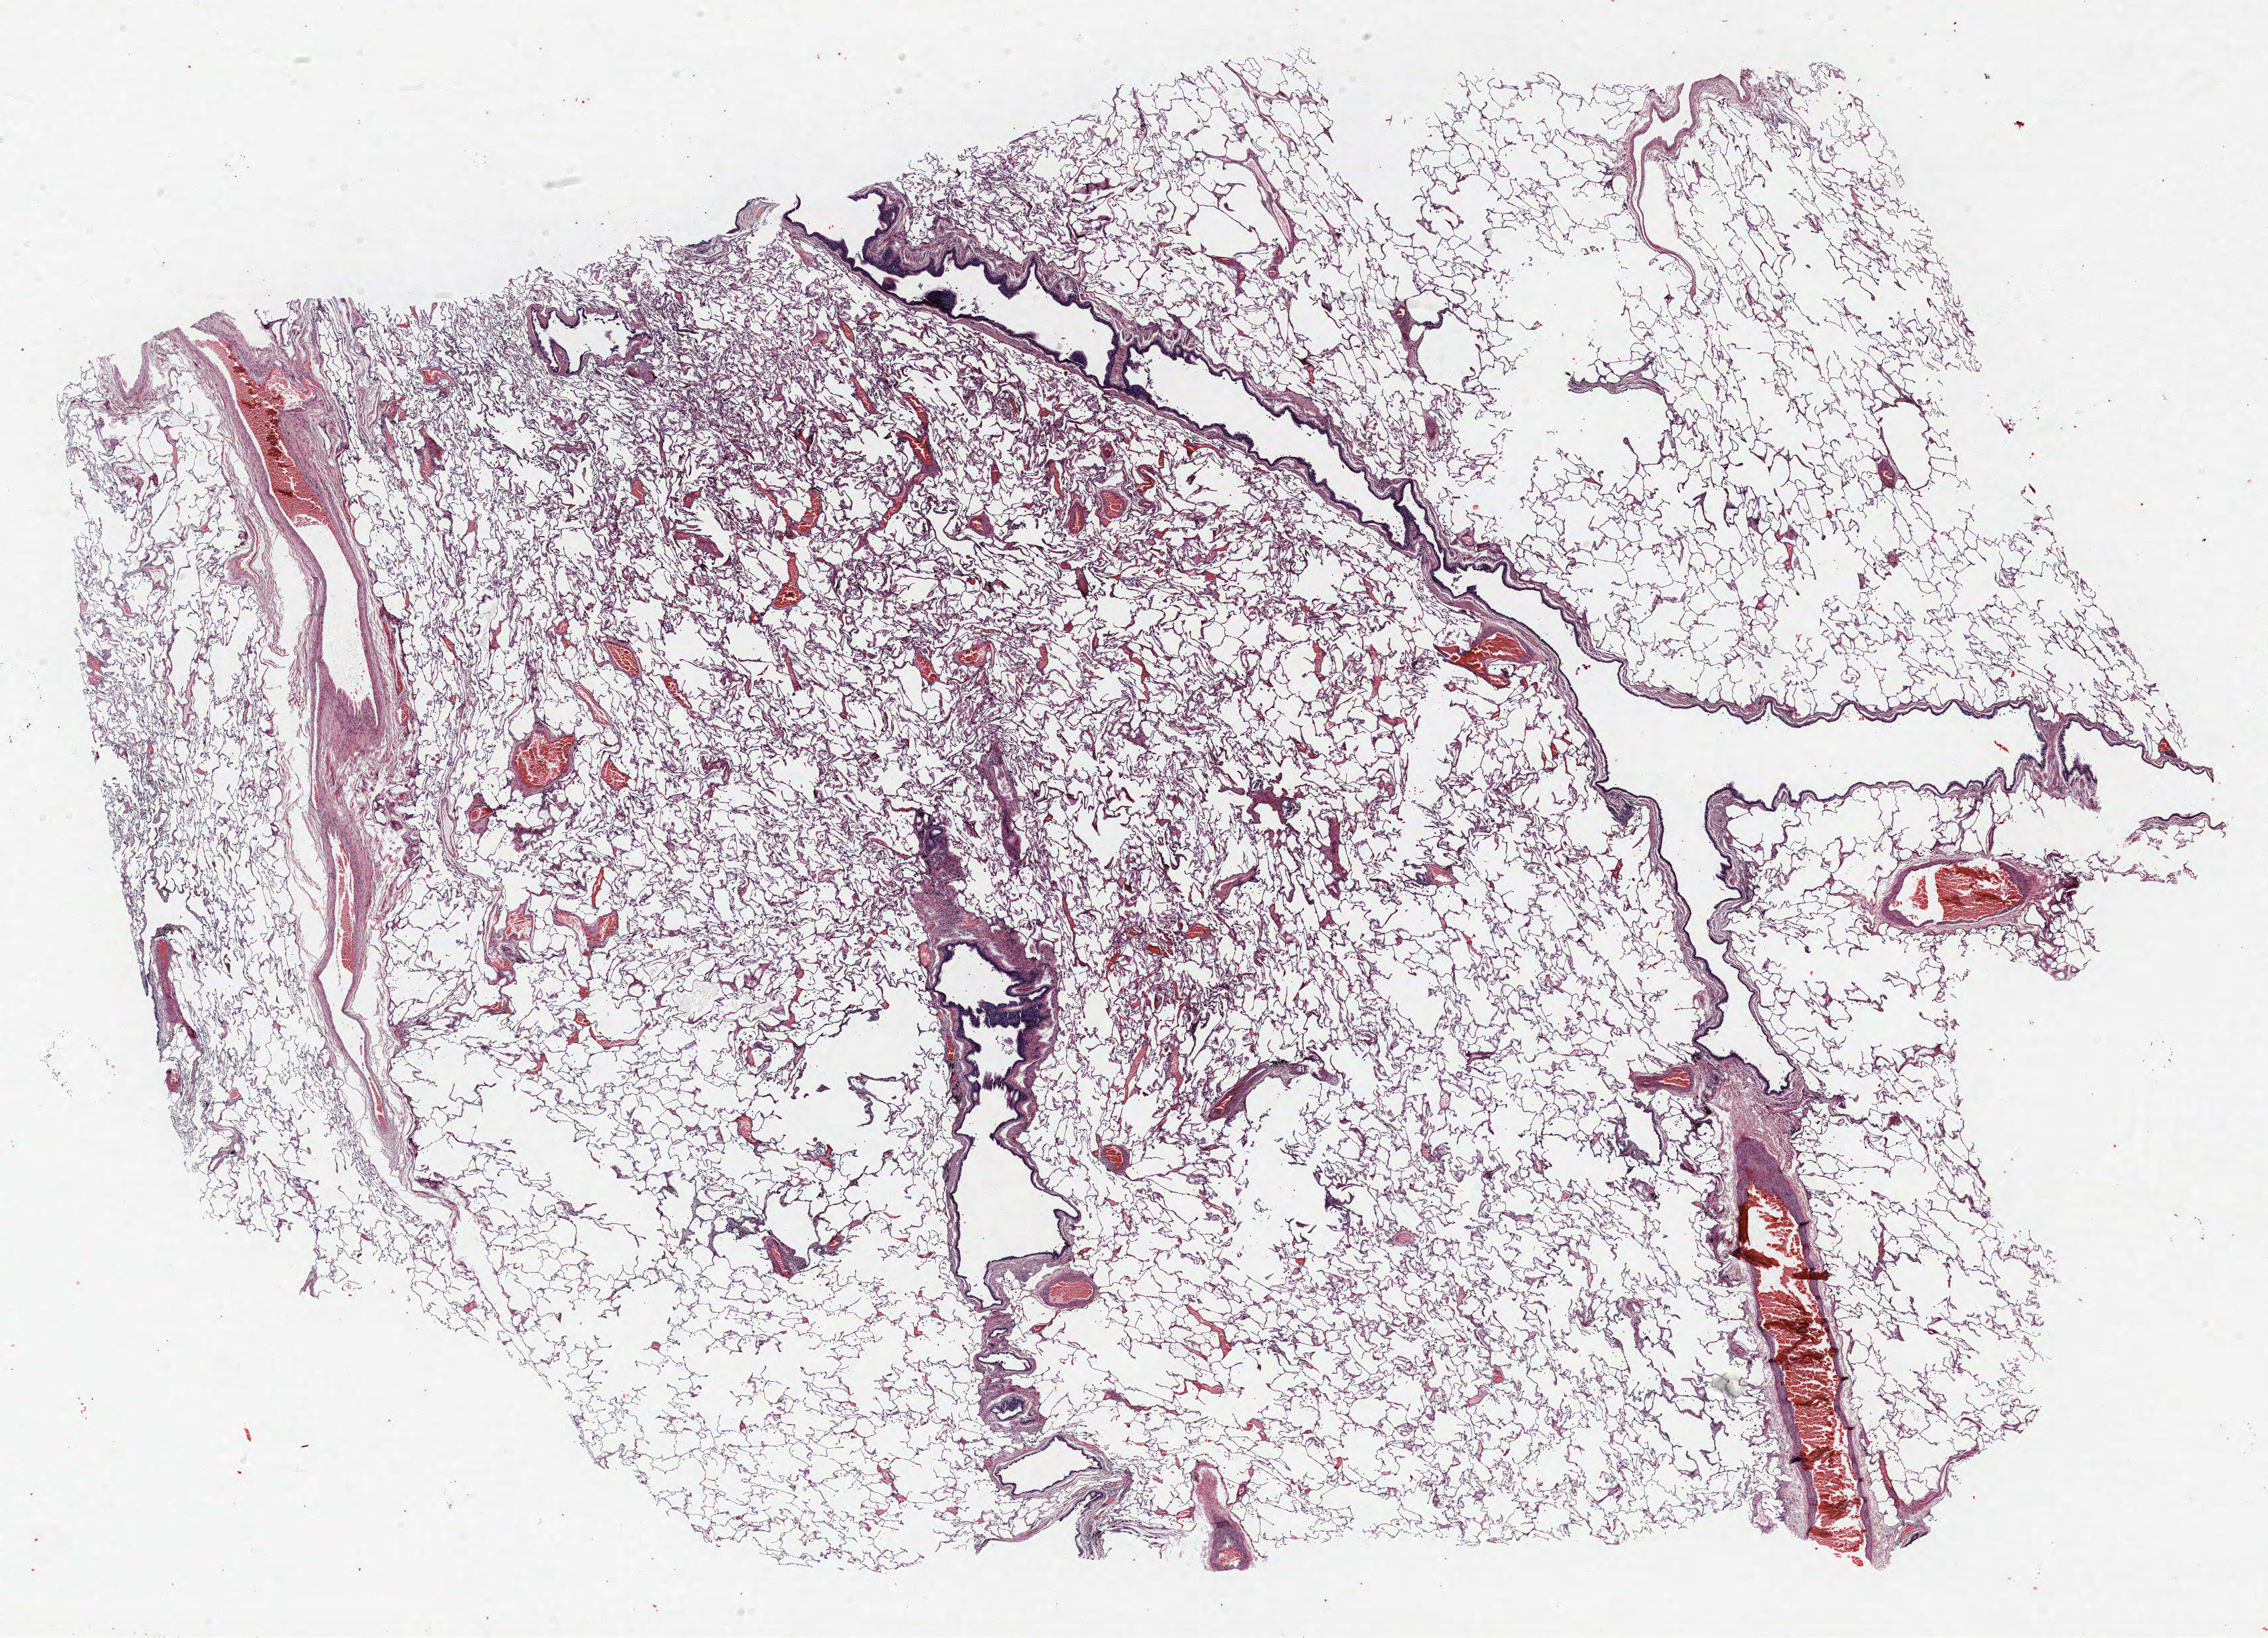
Whole-slide histology image, H&E, low-resolution overview of the scanned area, about 27.1 x 19.6 mm; formalin-fixed paraffin-embedded (FFPE) section; lung. Male patient, aged 62 at enrolment. Grade: well differentiated (G1).
Tumour size (pathology): 15 mm. Stage (AJCC 6th edition): IA. Primary tumour location (clinical record): left upper lobe. Participant's lung-cancer diagnosis: Squamous cell carcinoma, NOS (ICD-O-3 8070/3). Note: participant had 2 primary lung cancers recorded; fields above describe the first.